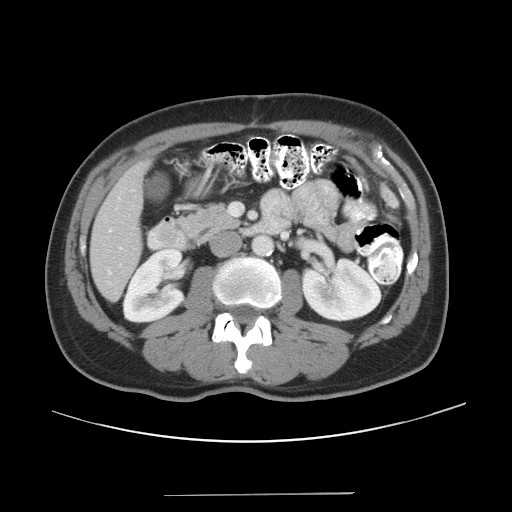
Contrast-enhanced abdominal CT, one axial slice. Slice 13 of 43 in the series (ordered by position). Reconstruction kernel STANDARD. 120 kVp. Intravenous contrast given. Soft-tissue window (W 400 / L 40 HU). 5 mm slice thickness. 512 × 512 image matrix, field of view 409 × 409 mm. Male patient, age 65 years. Case-level facts recorded for this patient, not image findings: diagnosis: colorectal cancer liver metastases, imaged before liver resection; multiple liver metastases: no; largest metastasis: 3.8 cm; disease in both lobes: no.
Outlined on this slice (outlined manually by an expert reader):
- hepatic veins: bounding box [x1, y1, x2, y2] px = [108, 271, 111, 274]
- liver: [91, 164, 145, 300]
- planned liver remnant (the part of the liver to remain after resection): [91, 164, 145, 300]